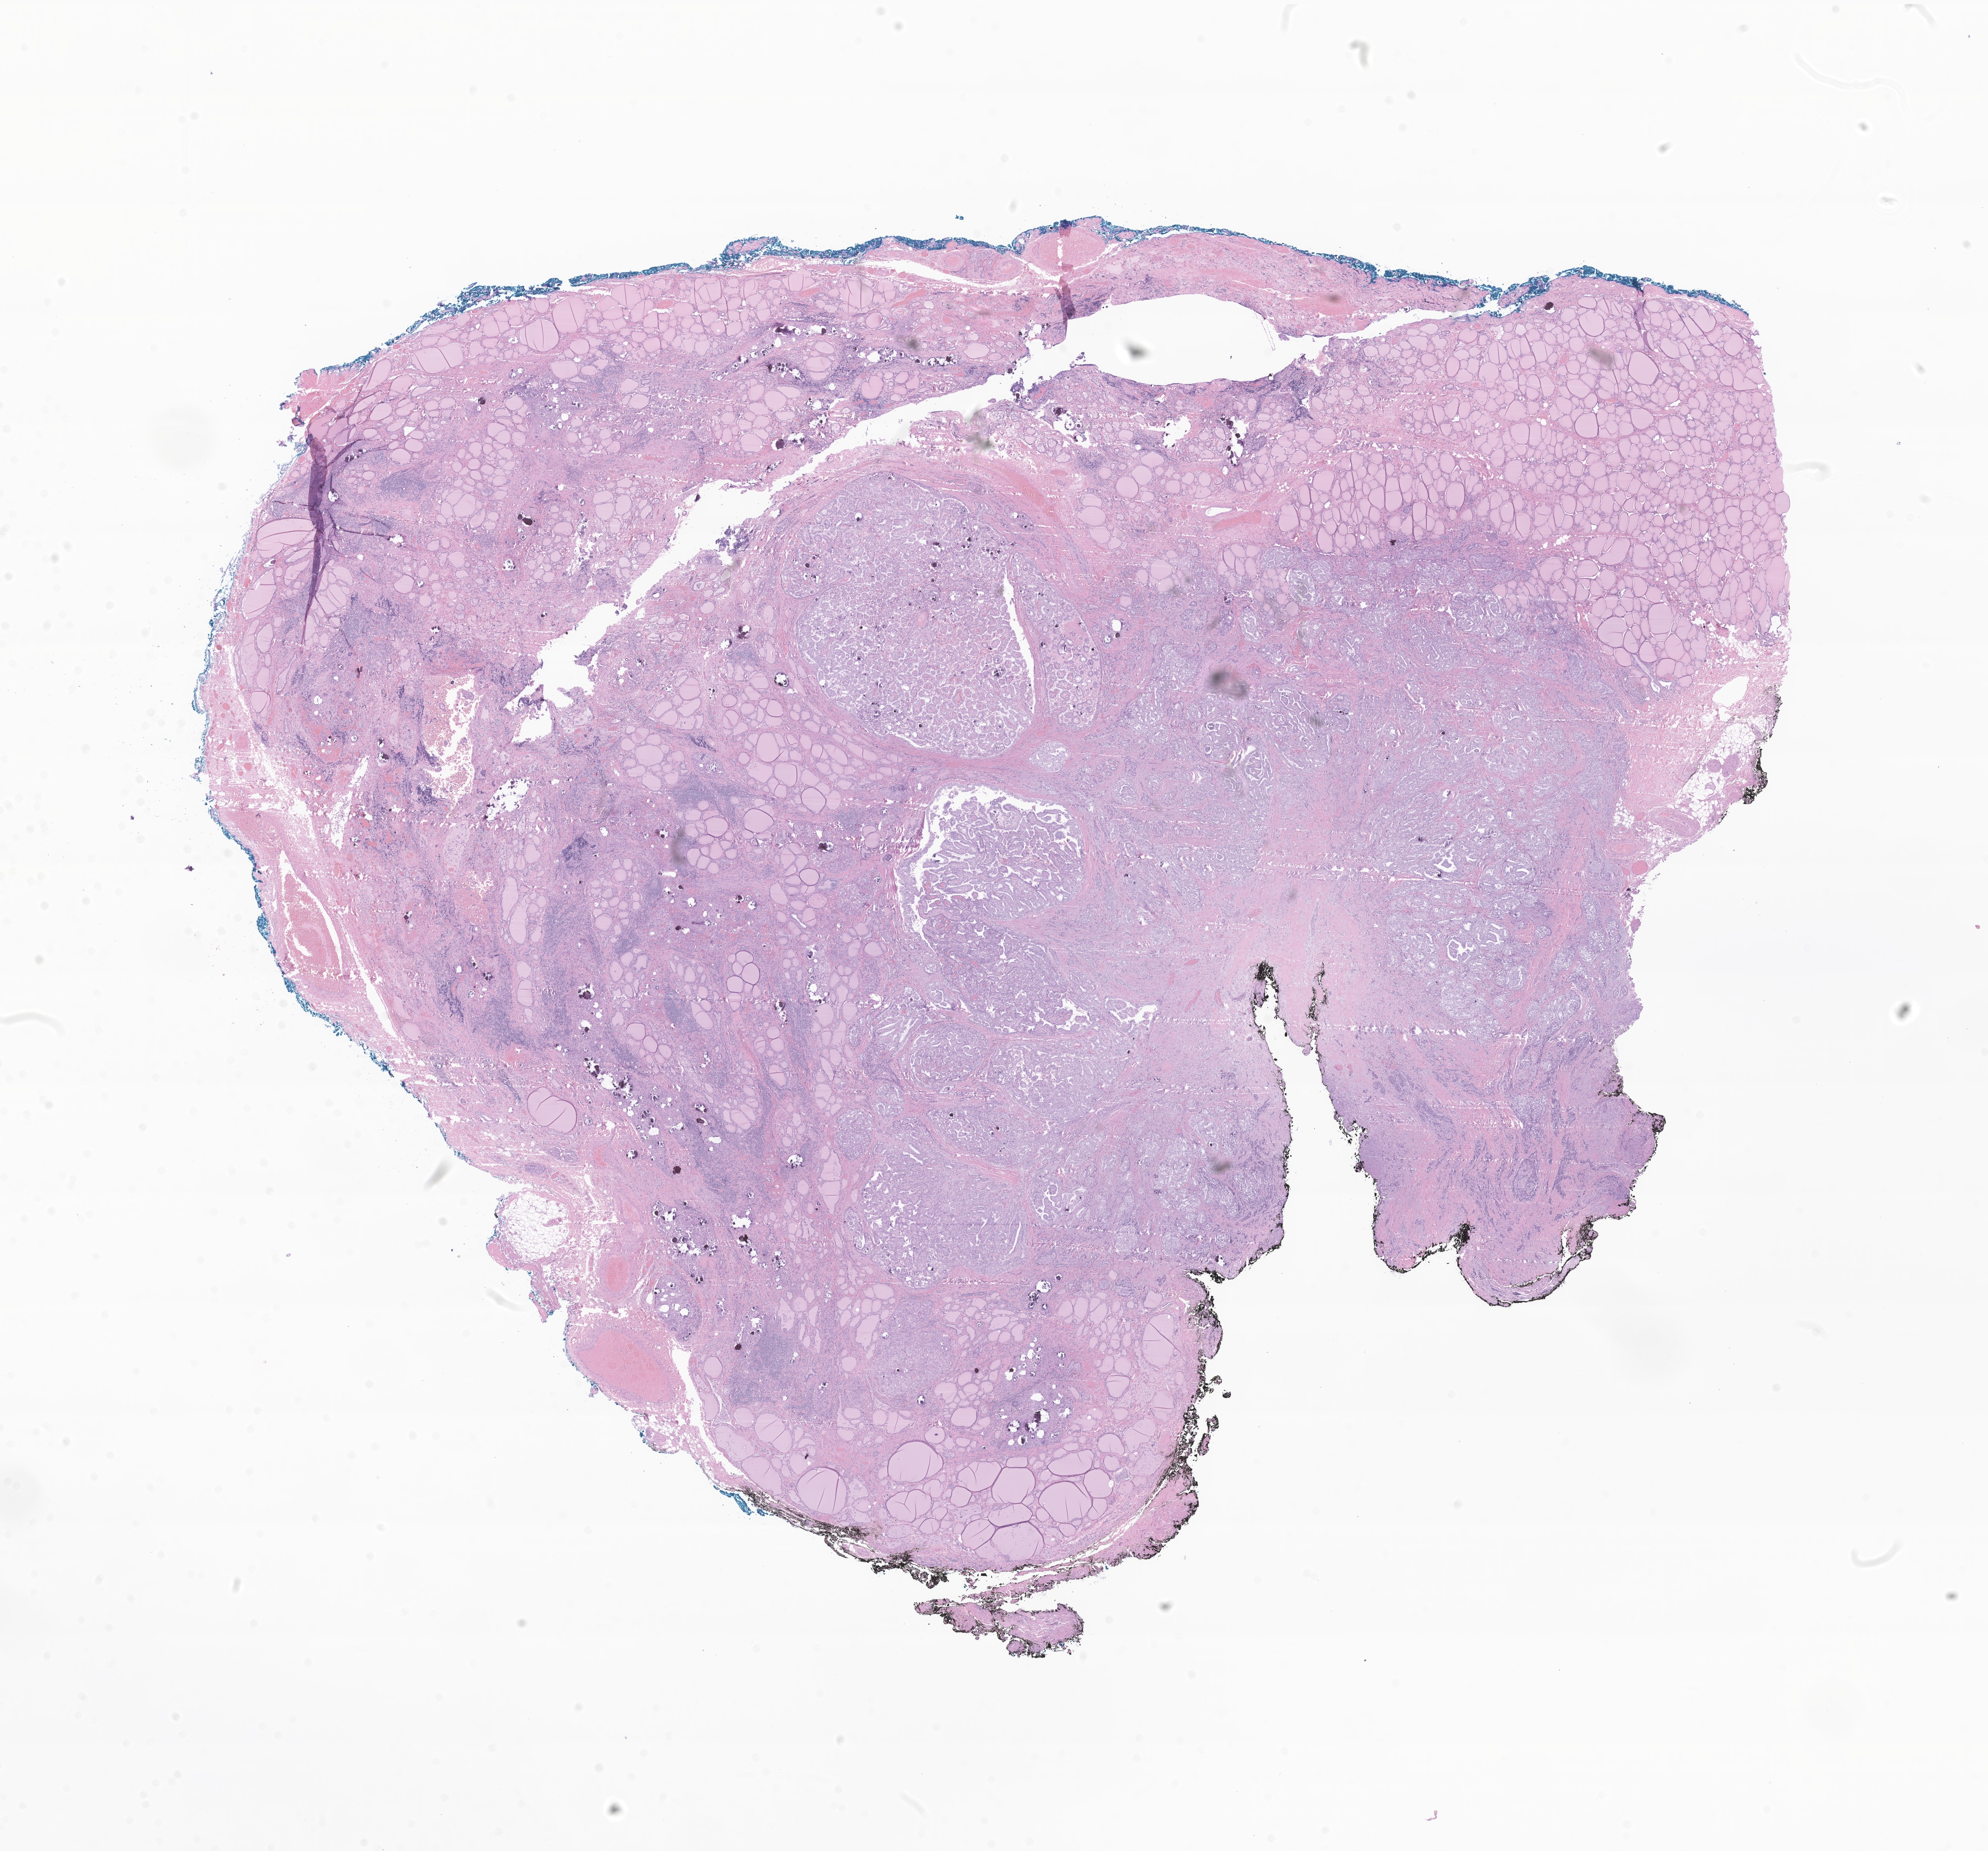
H&E whole-slide image of tumor tissue from the thyroid — low-resolution overview of the scanned area, about 19.3 x 18.0 mm, formalin-fixed paraffin-embedded section. Patient: male, age 99 months (8 years 3 months).
Diagnosis: Papillary carcinoma, NOS.